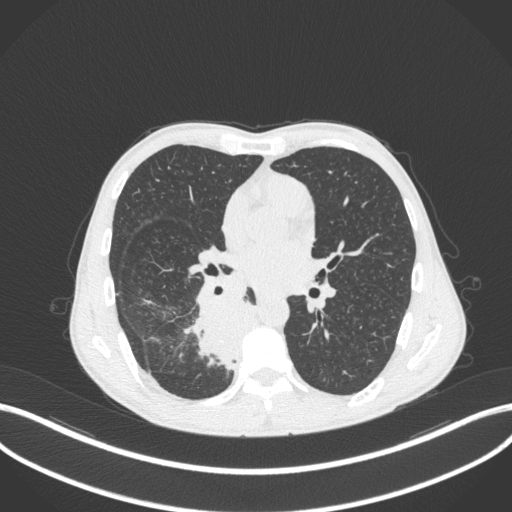
Chest CT, one axial slice. Slice 190 of 371 in the series (ordered by position). Lung window (W 1500 / L -600 HU). 1 mm slice thickness. 512 × 512 image matrix. Male patient, age 58 years. Case-level facts recorded for this patient, not image findings: clinical TNM (as recorded): T3 N1 M1.
Structures marked on this image (rectangle marked by the reading radiologist):
- lung tumour (recorded histology: squamous cell carcinoma): box from (x=188, y=296) to (x=259, y=370) px